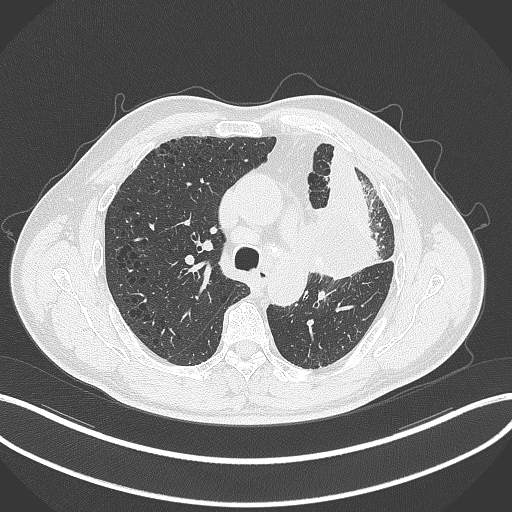
Chest CT, one axial slice; slice 207 of 297 in the series (ordered by position); 120 kVp; lung window (W 1500 / L -600 HU); 512 × 512 image matrix, field of view 400 × 400 mm. Male patient, age 68 years. Case-level facts recorded for this patient, not image findings: clinical TNM (as recorded): T3 N3 M1.
Outlined on this slice (rectangle marked by the reading radiologist):
- lung tumour (recorded histology: adenocarcinoma): bounding box <308,181,387,287> (left, top, right, bottom; pixels)